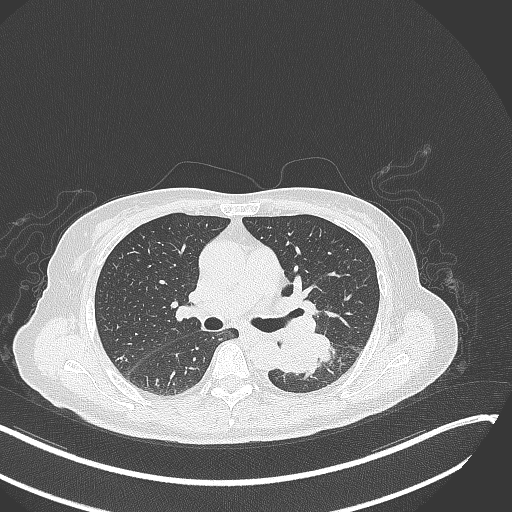
Chest CT, one axial slice. Slice 166 of 342 in the series (ordered by position). Reconstruction kernel B70f. Lung window (W 1500 / L -600 HU). 1 mm slice thickness. 512 × 512 image matrix. Patient: female, 64 years. From the clinical record (not read from this slice): clinical TNM (as recorded): T3 N1 M1; histopathological grade: G3.
Structures marked on this image (rectangle marked by the reading radiologist):
- lung tumour (recorded histology: small cell carcinoma): box from (x=276, y=334) to (x=336, y=378) px